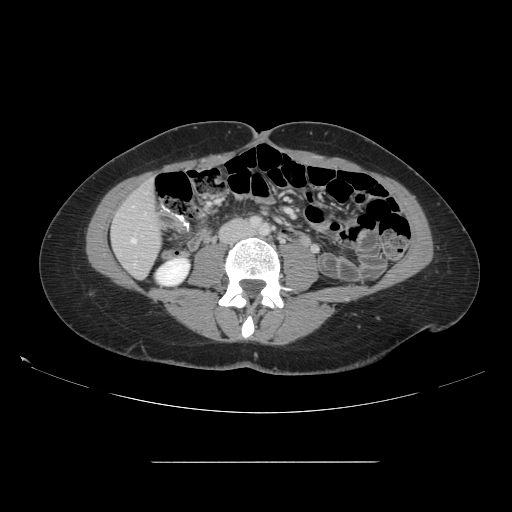
Contrast-enhanced abdominal CT, one axial slice; slice 30 of 151 in the series (ordered by position); soft-tissue window (W 400 / L 40 HU); 512 × 512 image matrix, field of view 421 × 421 mm. Female patient, age 46 years. From the clinical record (not read from this slice): diagnosis: colorectal cancer liver metastases, imaged before liver resection; multiple liver metastases: yes; largest metastasis: 3 cm; disease in both lobes: yes.
Outlined on this slice (expert manual segmentation):
- hepatic veins: bounding box [x1, y1, x2, y2] px = [131, 239, 135, 243]
- liver: [112, 183, 161, 278]
- planned liver remnant (the part of the liver to remain after resection): [112, 183, 161, 278]